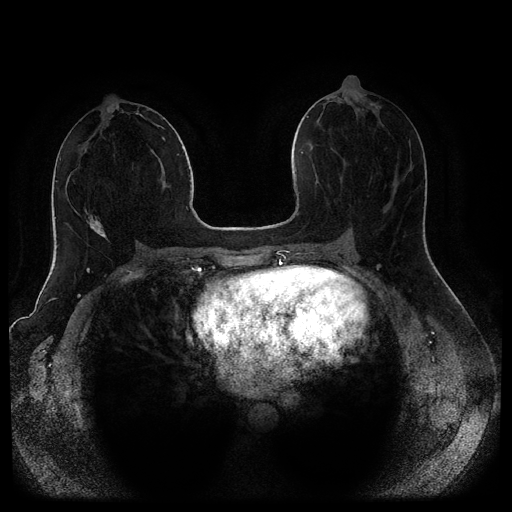
Breast MRI (dynamic contrast-enhanced, multi-phase), one axial slice; position 46 of 116 along the scan axis; dynamic contrast-enhanced series, time point 2 of 5 at this slice position (early post-contrast); 1.5 T; TE 2.6 ms, TR 5.3 ms; 2 mm slice thickness; 512 × 512 image matrix, field of view 370 × 370 mm. Female patient, age 44 years.
Structures marked on this image (semi-automatic segmentation, software-assisted and operator-edited):
- breast lesion (labelled benign in the annotation): bounding box [x1, y1, x2, y2] px = [87, 217, 108, 240]